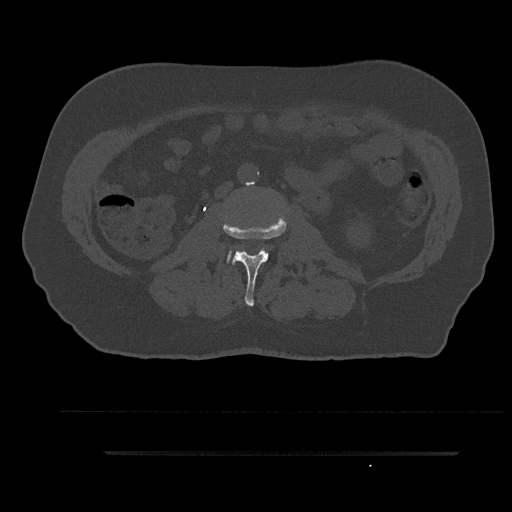
CT including the spine, one axial slice. Position 87 of 797 along the scan axis. Bone window (W 1800 / L 400 HU). 512 × 512 image matrix. Male patient, age 63 years. From the clinical record (not read from this slice): primary cancer: renal.
Structures marked on this image (semi-automatic segmentation, software-assisted and operator-edited):
- L2 vertebra: bounding box <222,214,287,306> (left, top, right, bottom; pixels)
- L3 vertebra: <227,251,242,262>